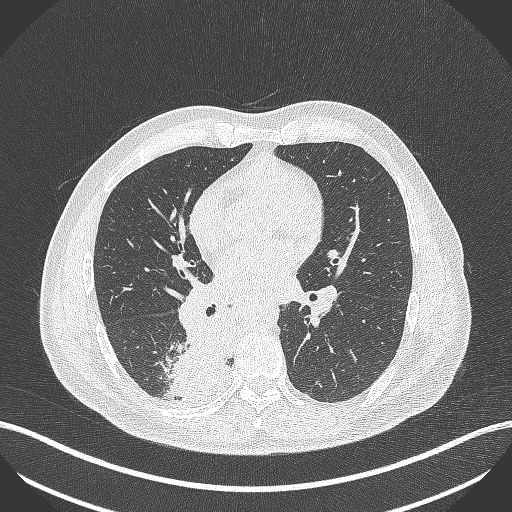
Chest CT, one axial slice; reconstruction kernel B70f; 100 kVp; lung window (W 1500 / L -600 HU); 1 mm slice thickness; 512 × 512 image matrix. Male patient, age 61 years. From the clinical record (not read from this slice): clinical TNM (as recorded): T1 N0 M0.
Structures marked on this image (bounding box drawn by a radiologist):
- lung tumour (recorded histology: small cell carcinoma): bounding box [x1, y1, x2, y2] px = [163, 316, 231, 403]